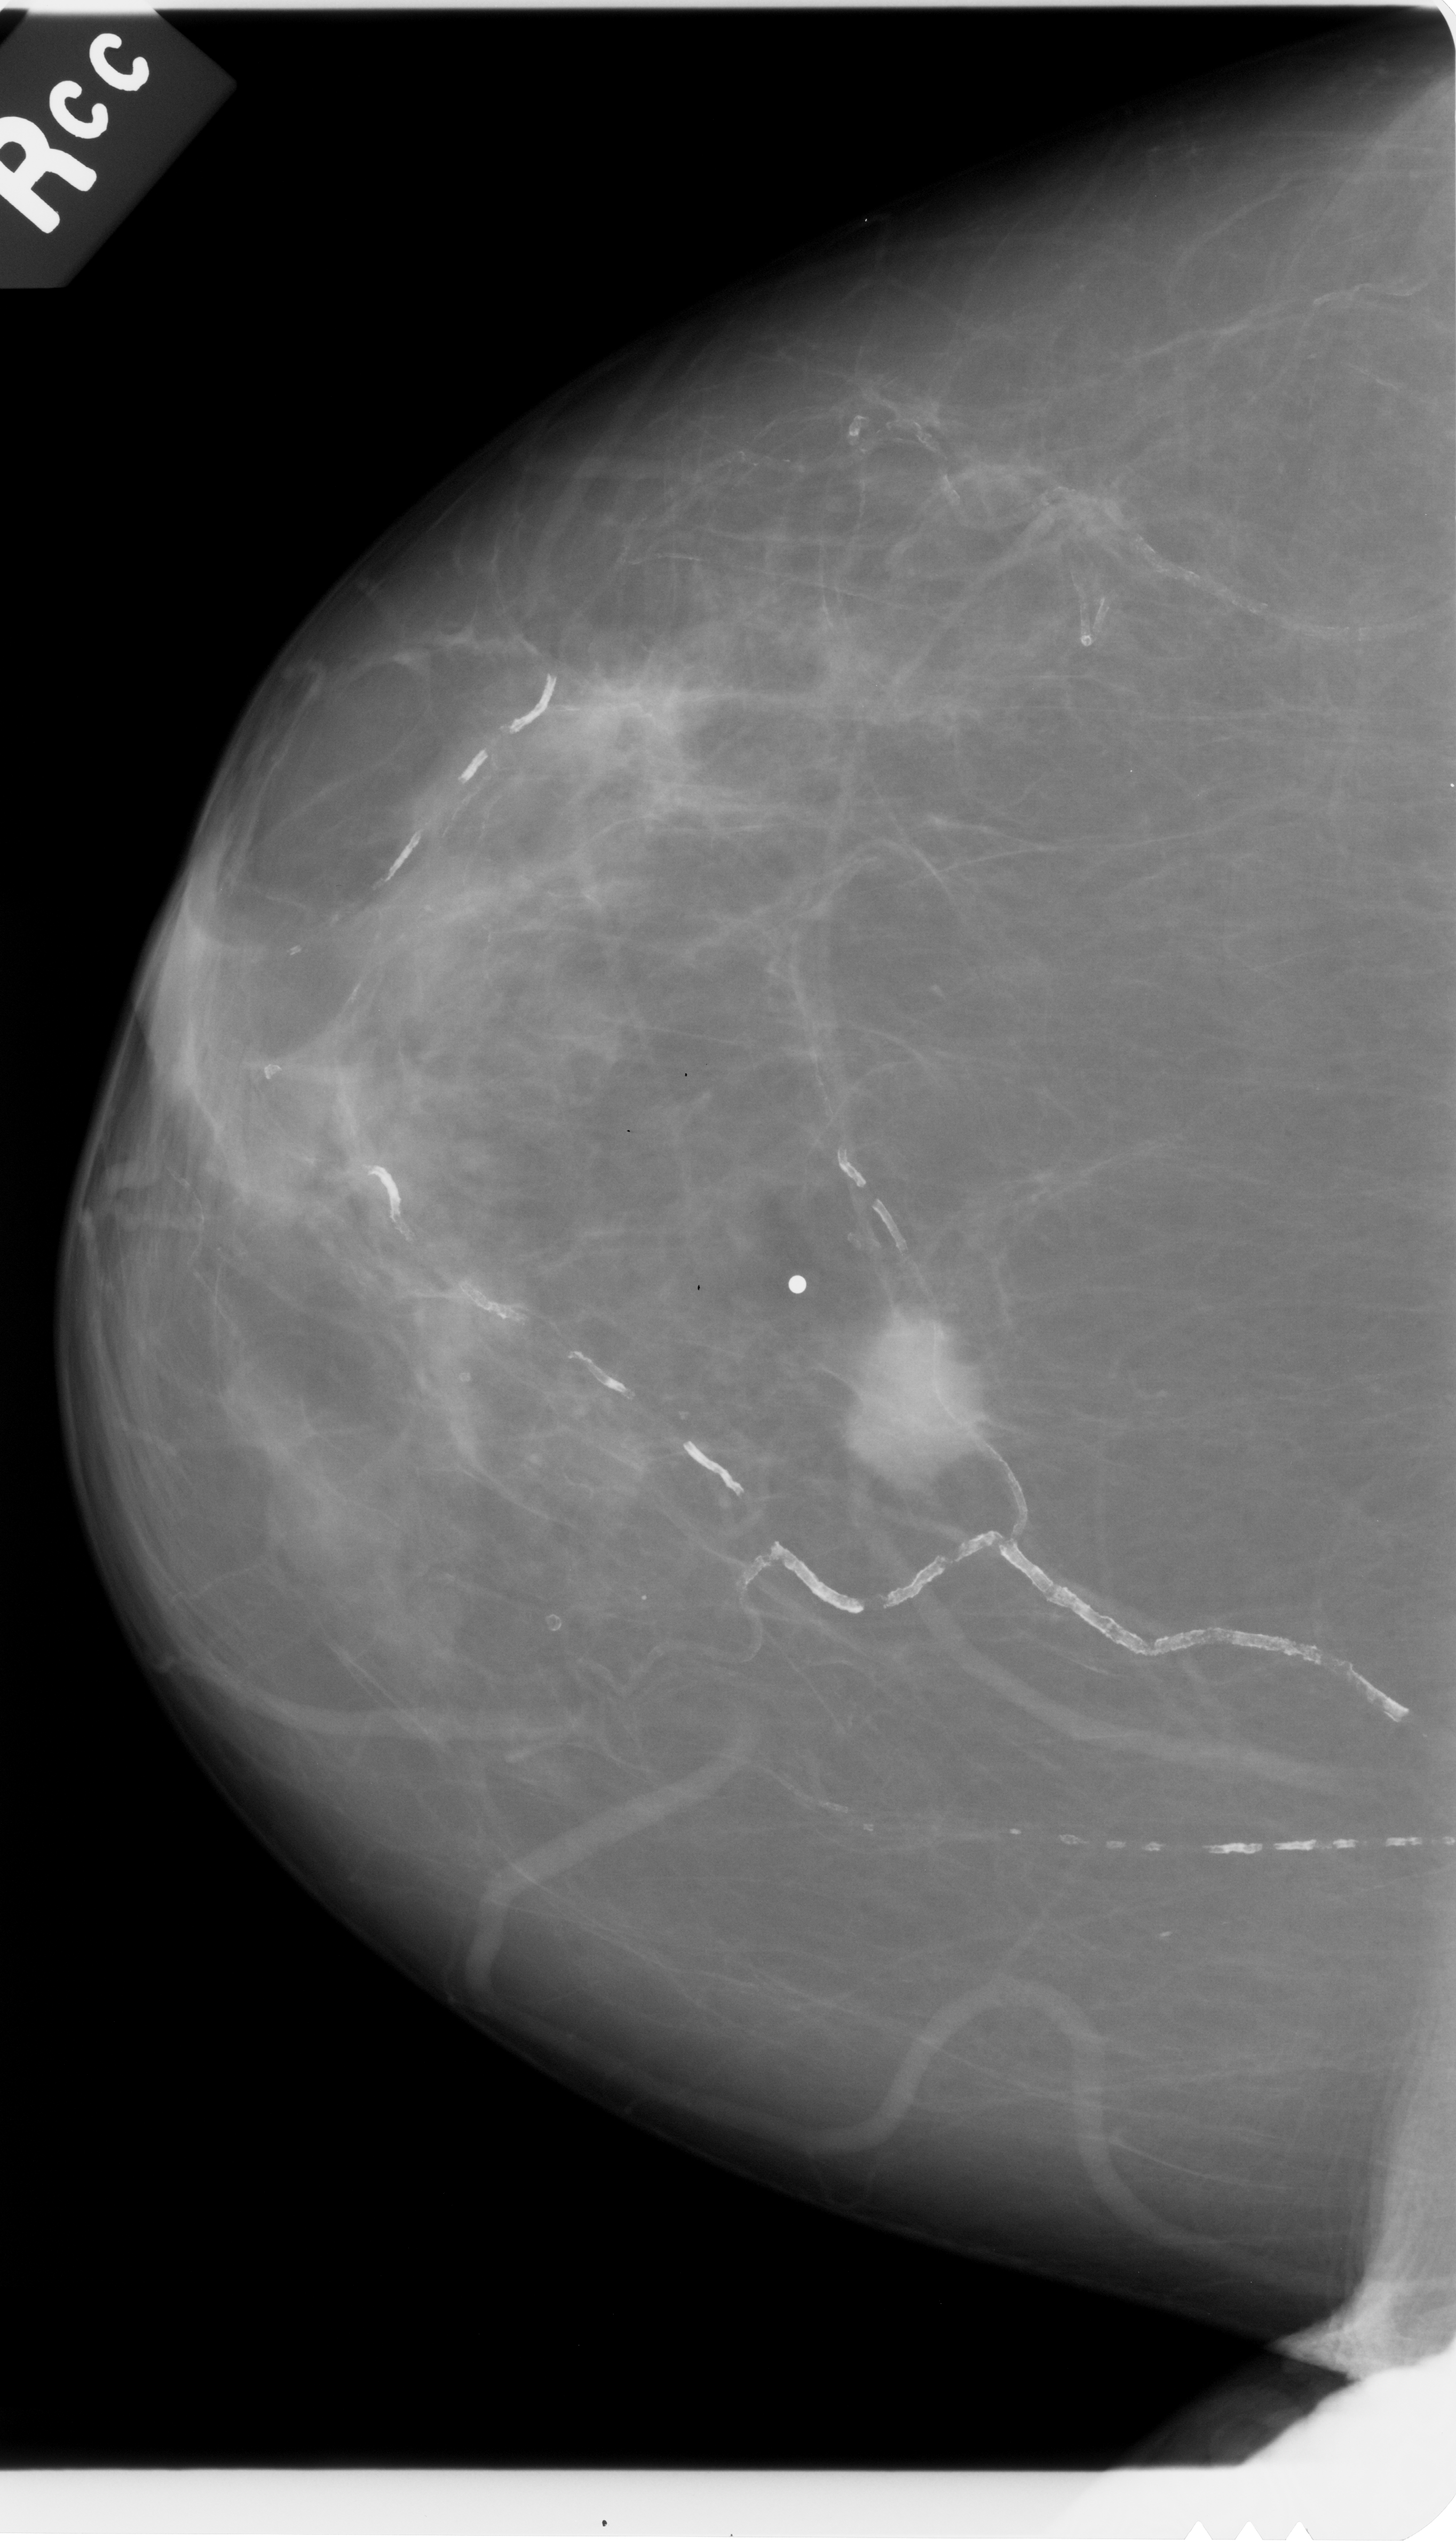
Mammogram (digitized film); right breast; CC view; breast composition: almost entirely fatty (BI-RADS density category 1 of 4).
Abnormality record for this image: mass, shape irregular, margins spiculated; BI-RADS assessment category 5; subtlety rating 5 on a 1 (subtle) to 5 (obvious) scale; pathology result (as recorded, not read from the image): malignant.